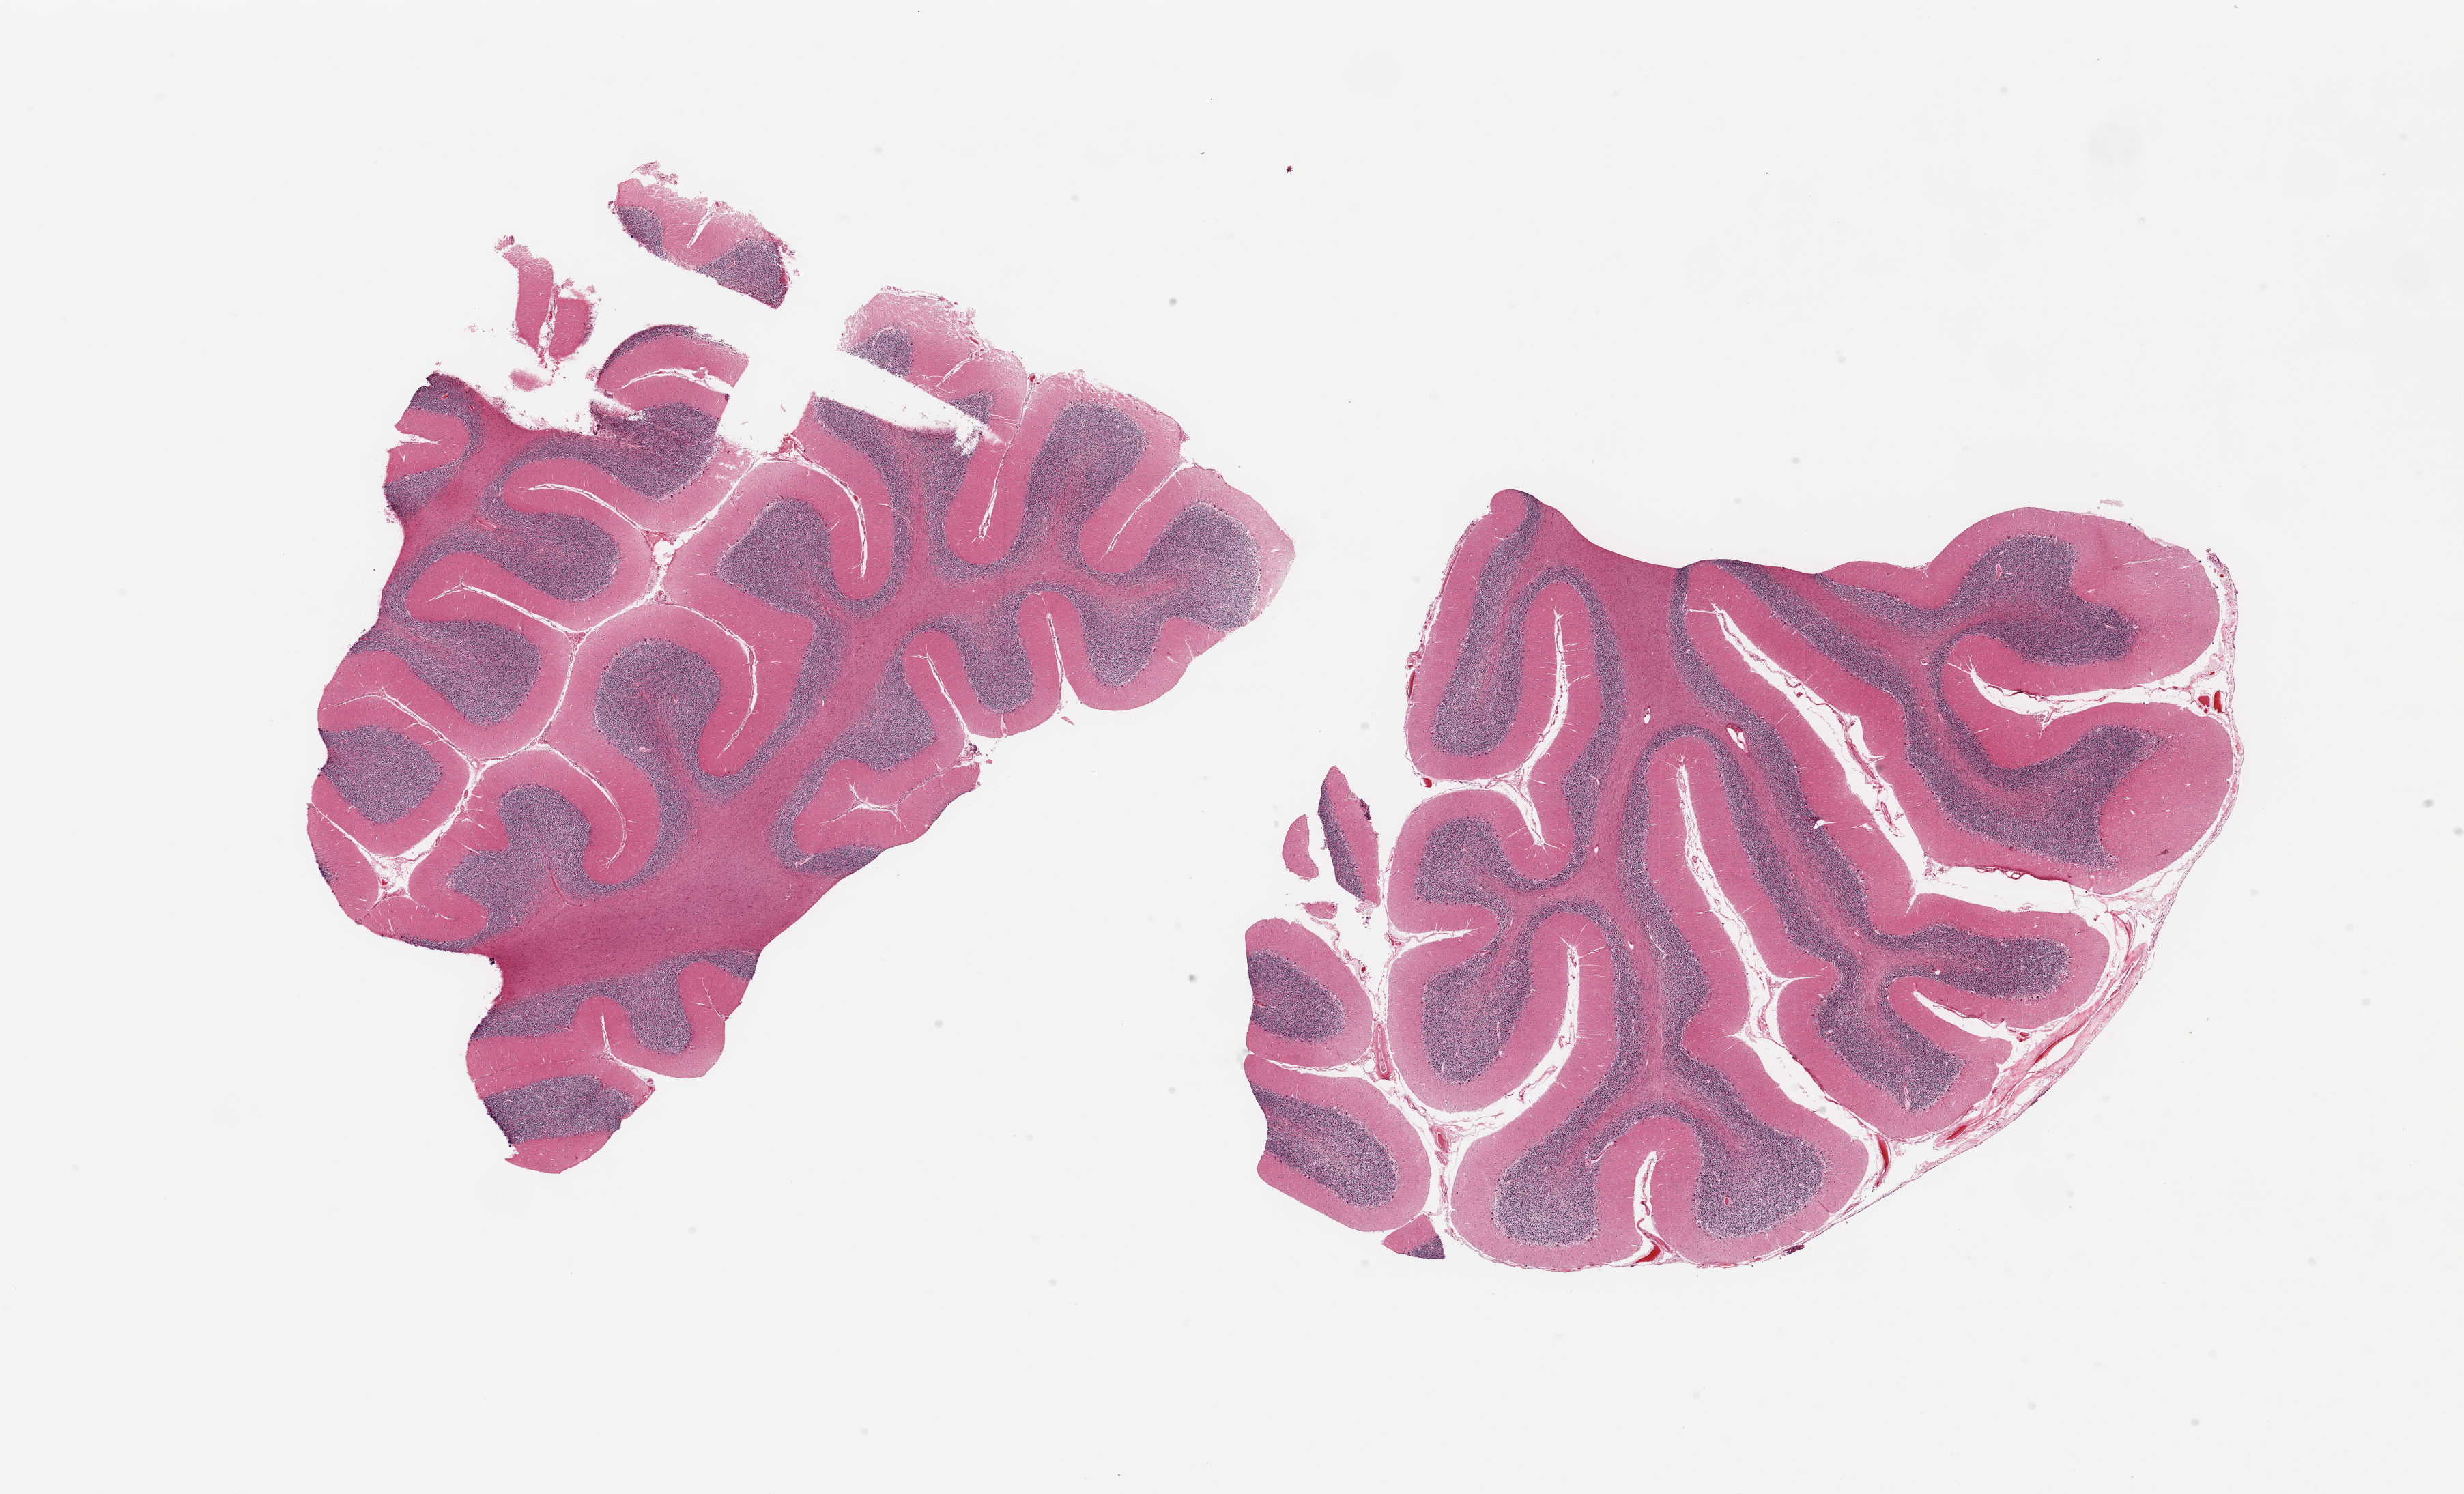
Whole-slide image, haematoxylin and eosin stain, low-resolution overview of the scanned area, about 28.5 x 17.3 mm. PAXgene-fixed, paraffin-embedded tissue. Section of cerebellum (target tissue). Tissue donor sample. Male donor.
- pathologist's review note for this sample: 2 pieces; one section contains meninges; Purkinje cells not depleted